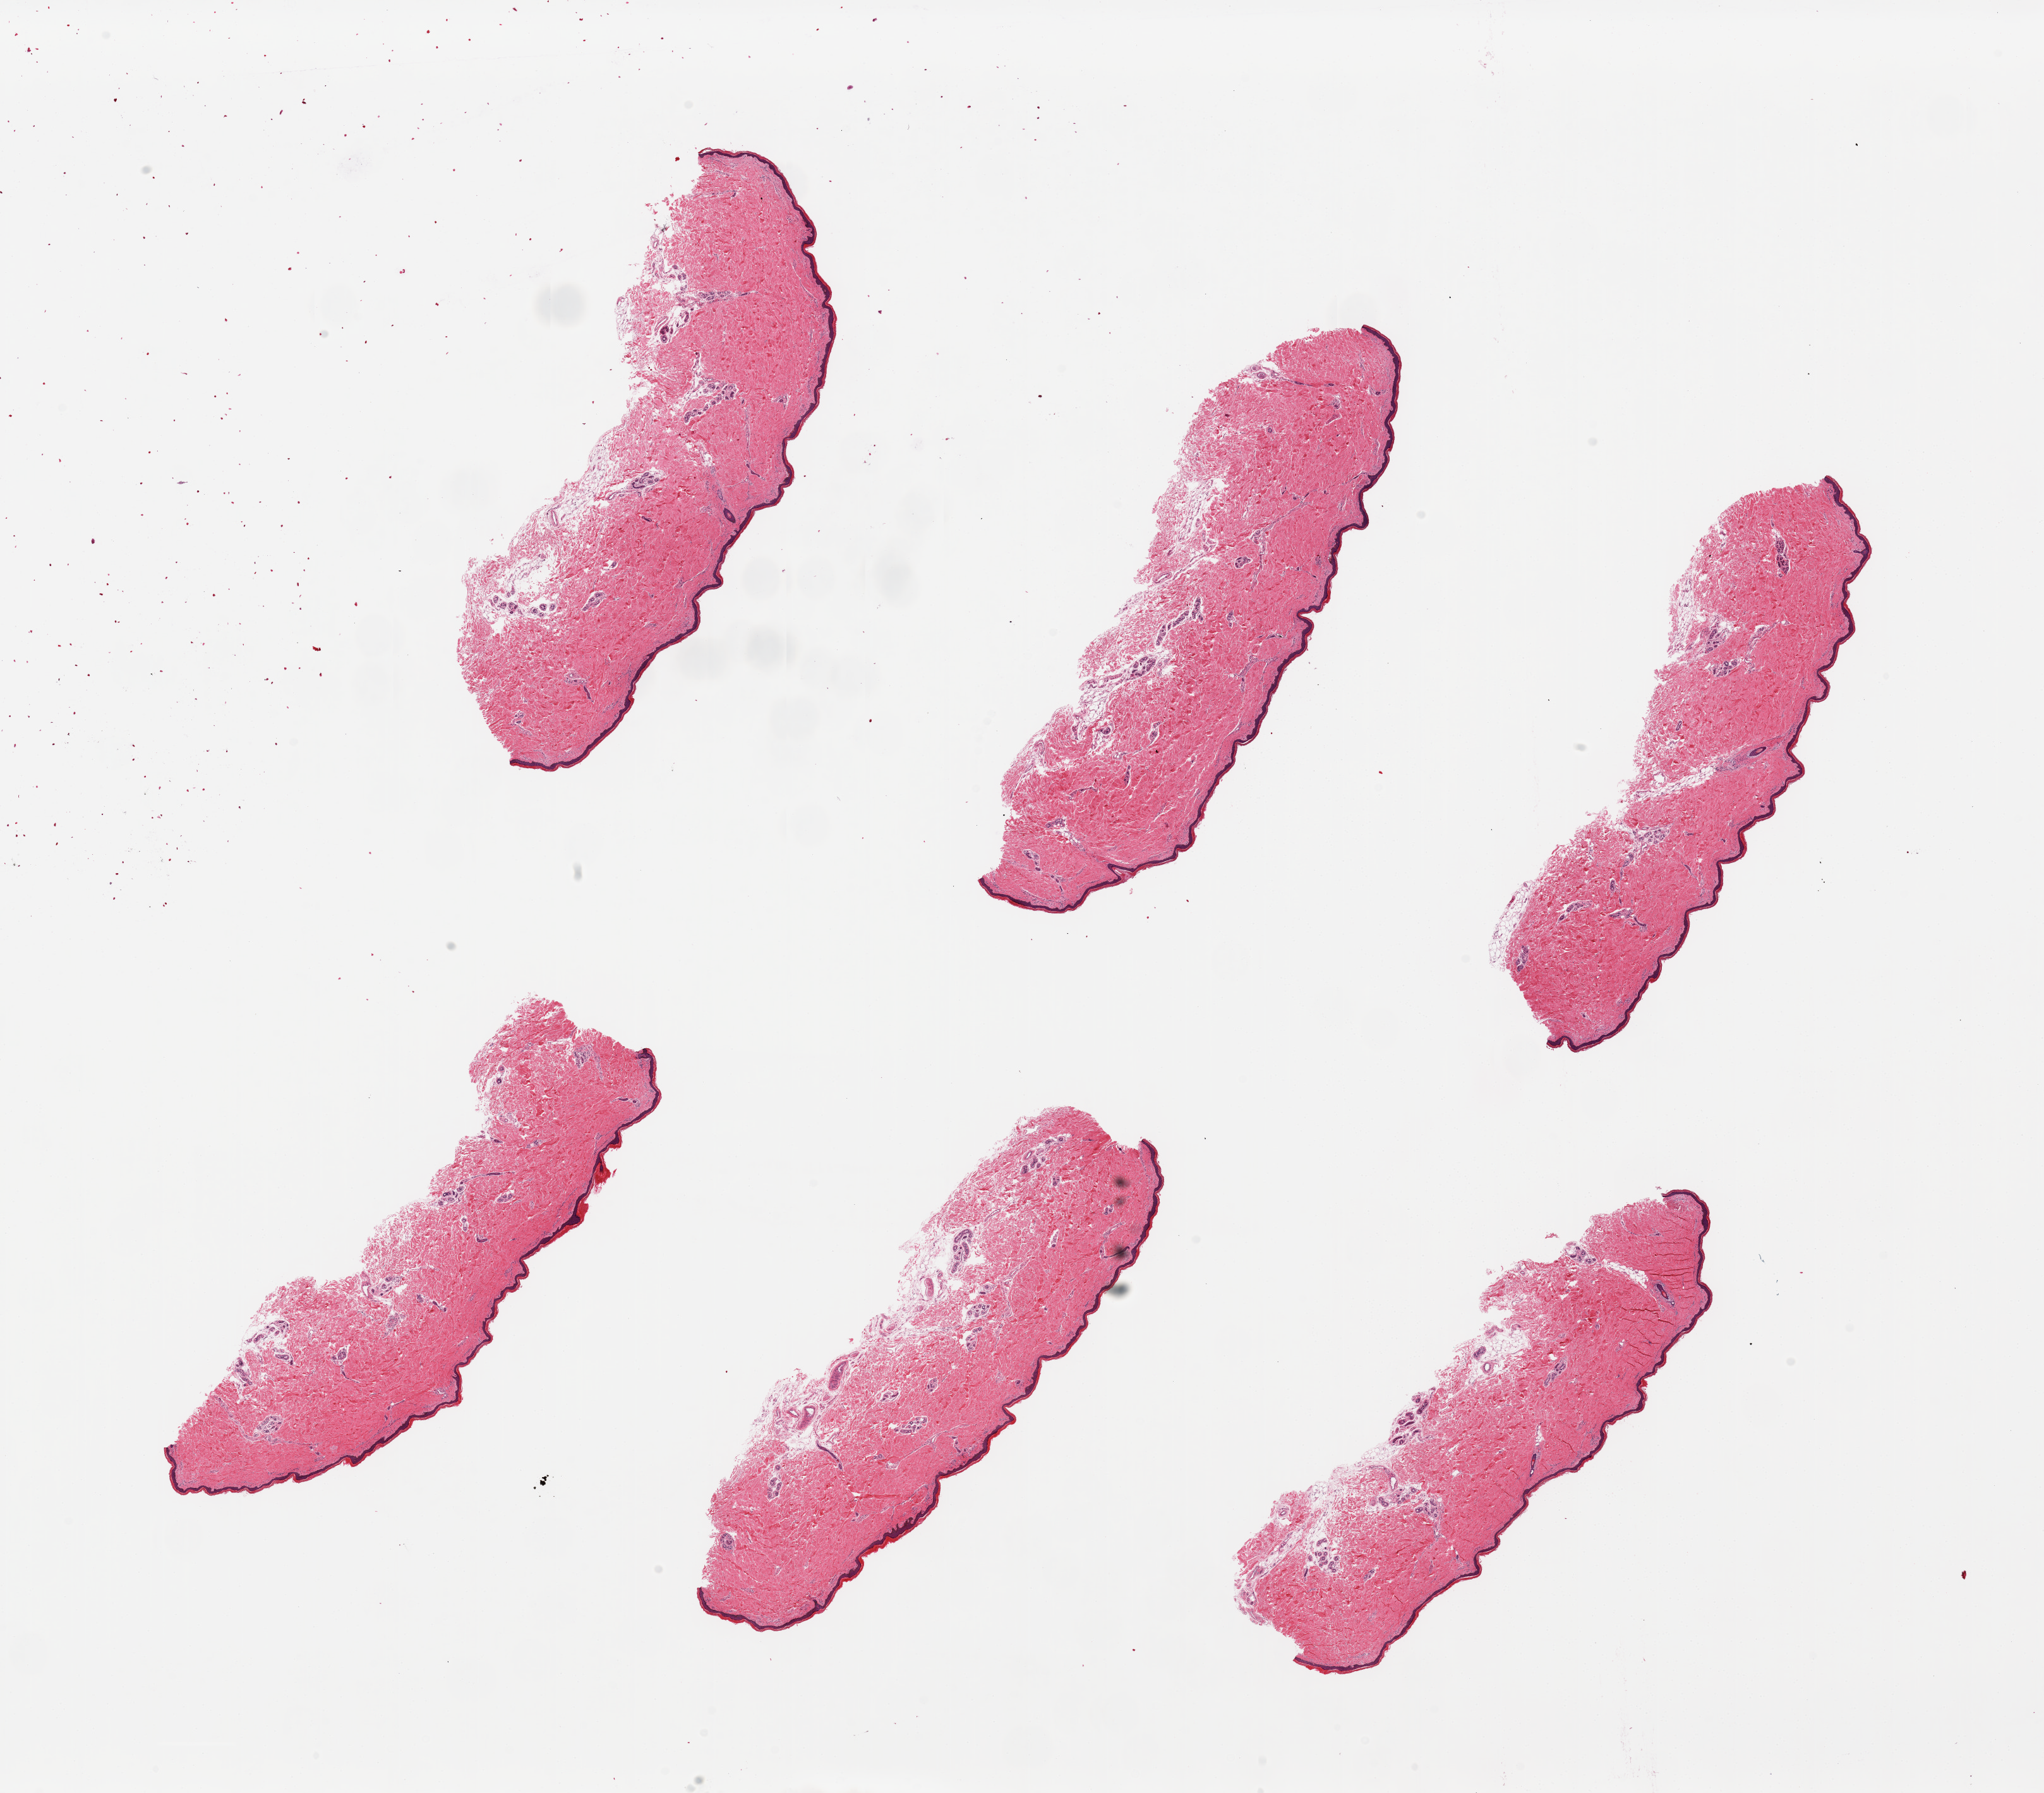
Whole-slide image, haematoxylin and eosin stain, shown as a low-resolution overview of the whole scanned area (about 25.6 x 22.4 mm); PAXgene-fixed paraffin-embedded (PFPE) section; sampled site (target tissue): skin of lower leg; donor tissue sample. Donor: female.
• review note (as recorded): 6 pieces, up to 8x3mm; subcutaneous adipose well trimmed